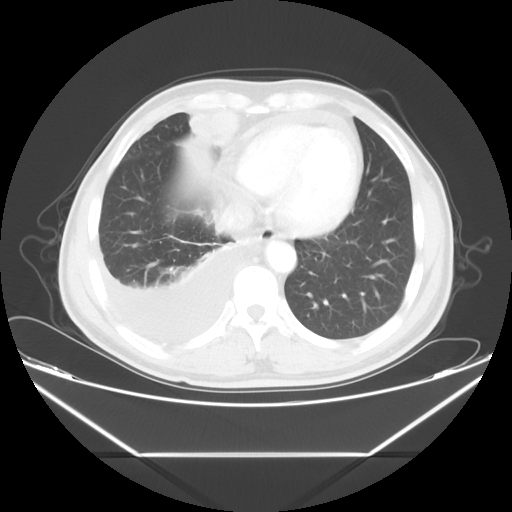
Chest CT, one axial slice; position 15 of 56 along the scan axis; reconstruction kernel STANDARD; 120 kVp; lung window (W 1500 / L -600 HU); 5 mm slice thickness; 512 × 512 image matrix. Patient: male, 57 years. From the clinical record (not read from this slice): clinical TNM (as recorded): T2 N3 M1.
Outlined on this slice (rectangle marked by the reading radiologist):
- lung tumour (recorded histology: adenocarcinoma): bounding box (x1, y1, x2, y2) in pixels: (186, 97, 239, 152)